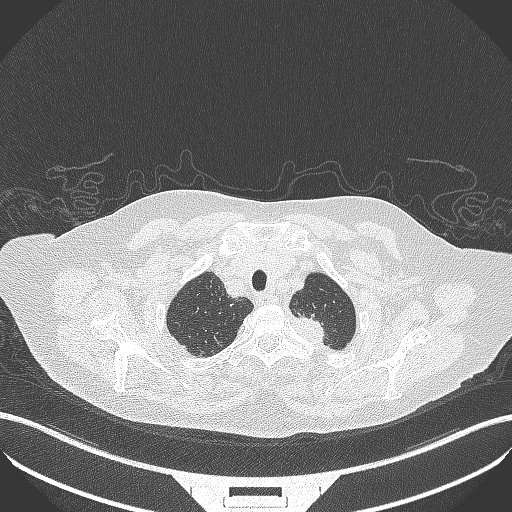
Chest CT, one axial slice; slice 307 of 353 in the series (ordered by position); 100 kVp; lung window (W 1500 / L -600 HU); 1 mm slice thickness; 512 × 512 image matrix. Female patient, age 81 years. From the clinical record (not read from this slice): clinical TNM (as recorded): T2a N0 M0.
Outlined on this slice (bounding box drawn by a radiologist):
- lung tumour (recorded histology: adenocarcinoma): box from (x=280, y=309) to (x=329, y=348) px